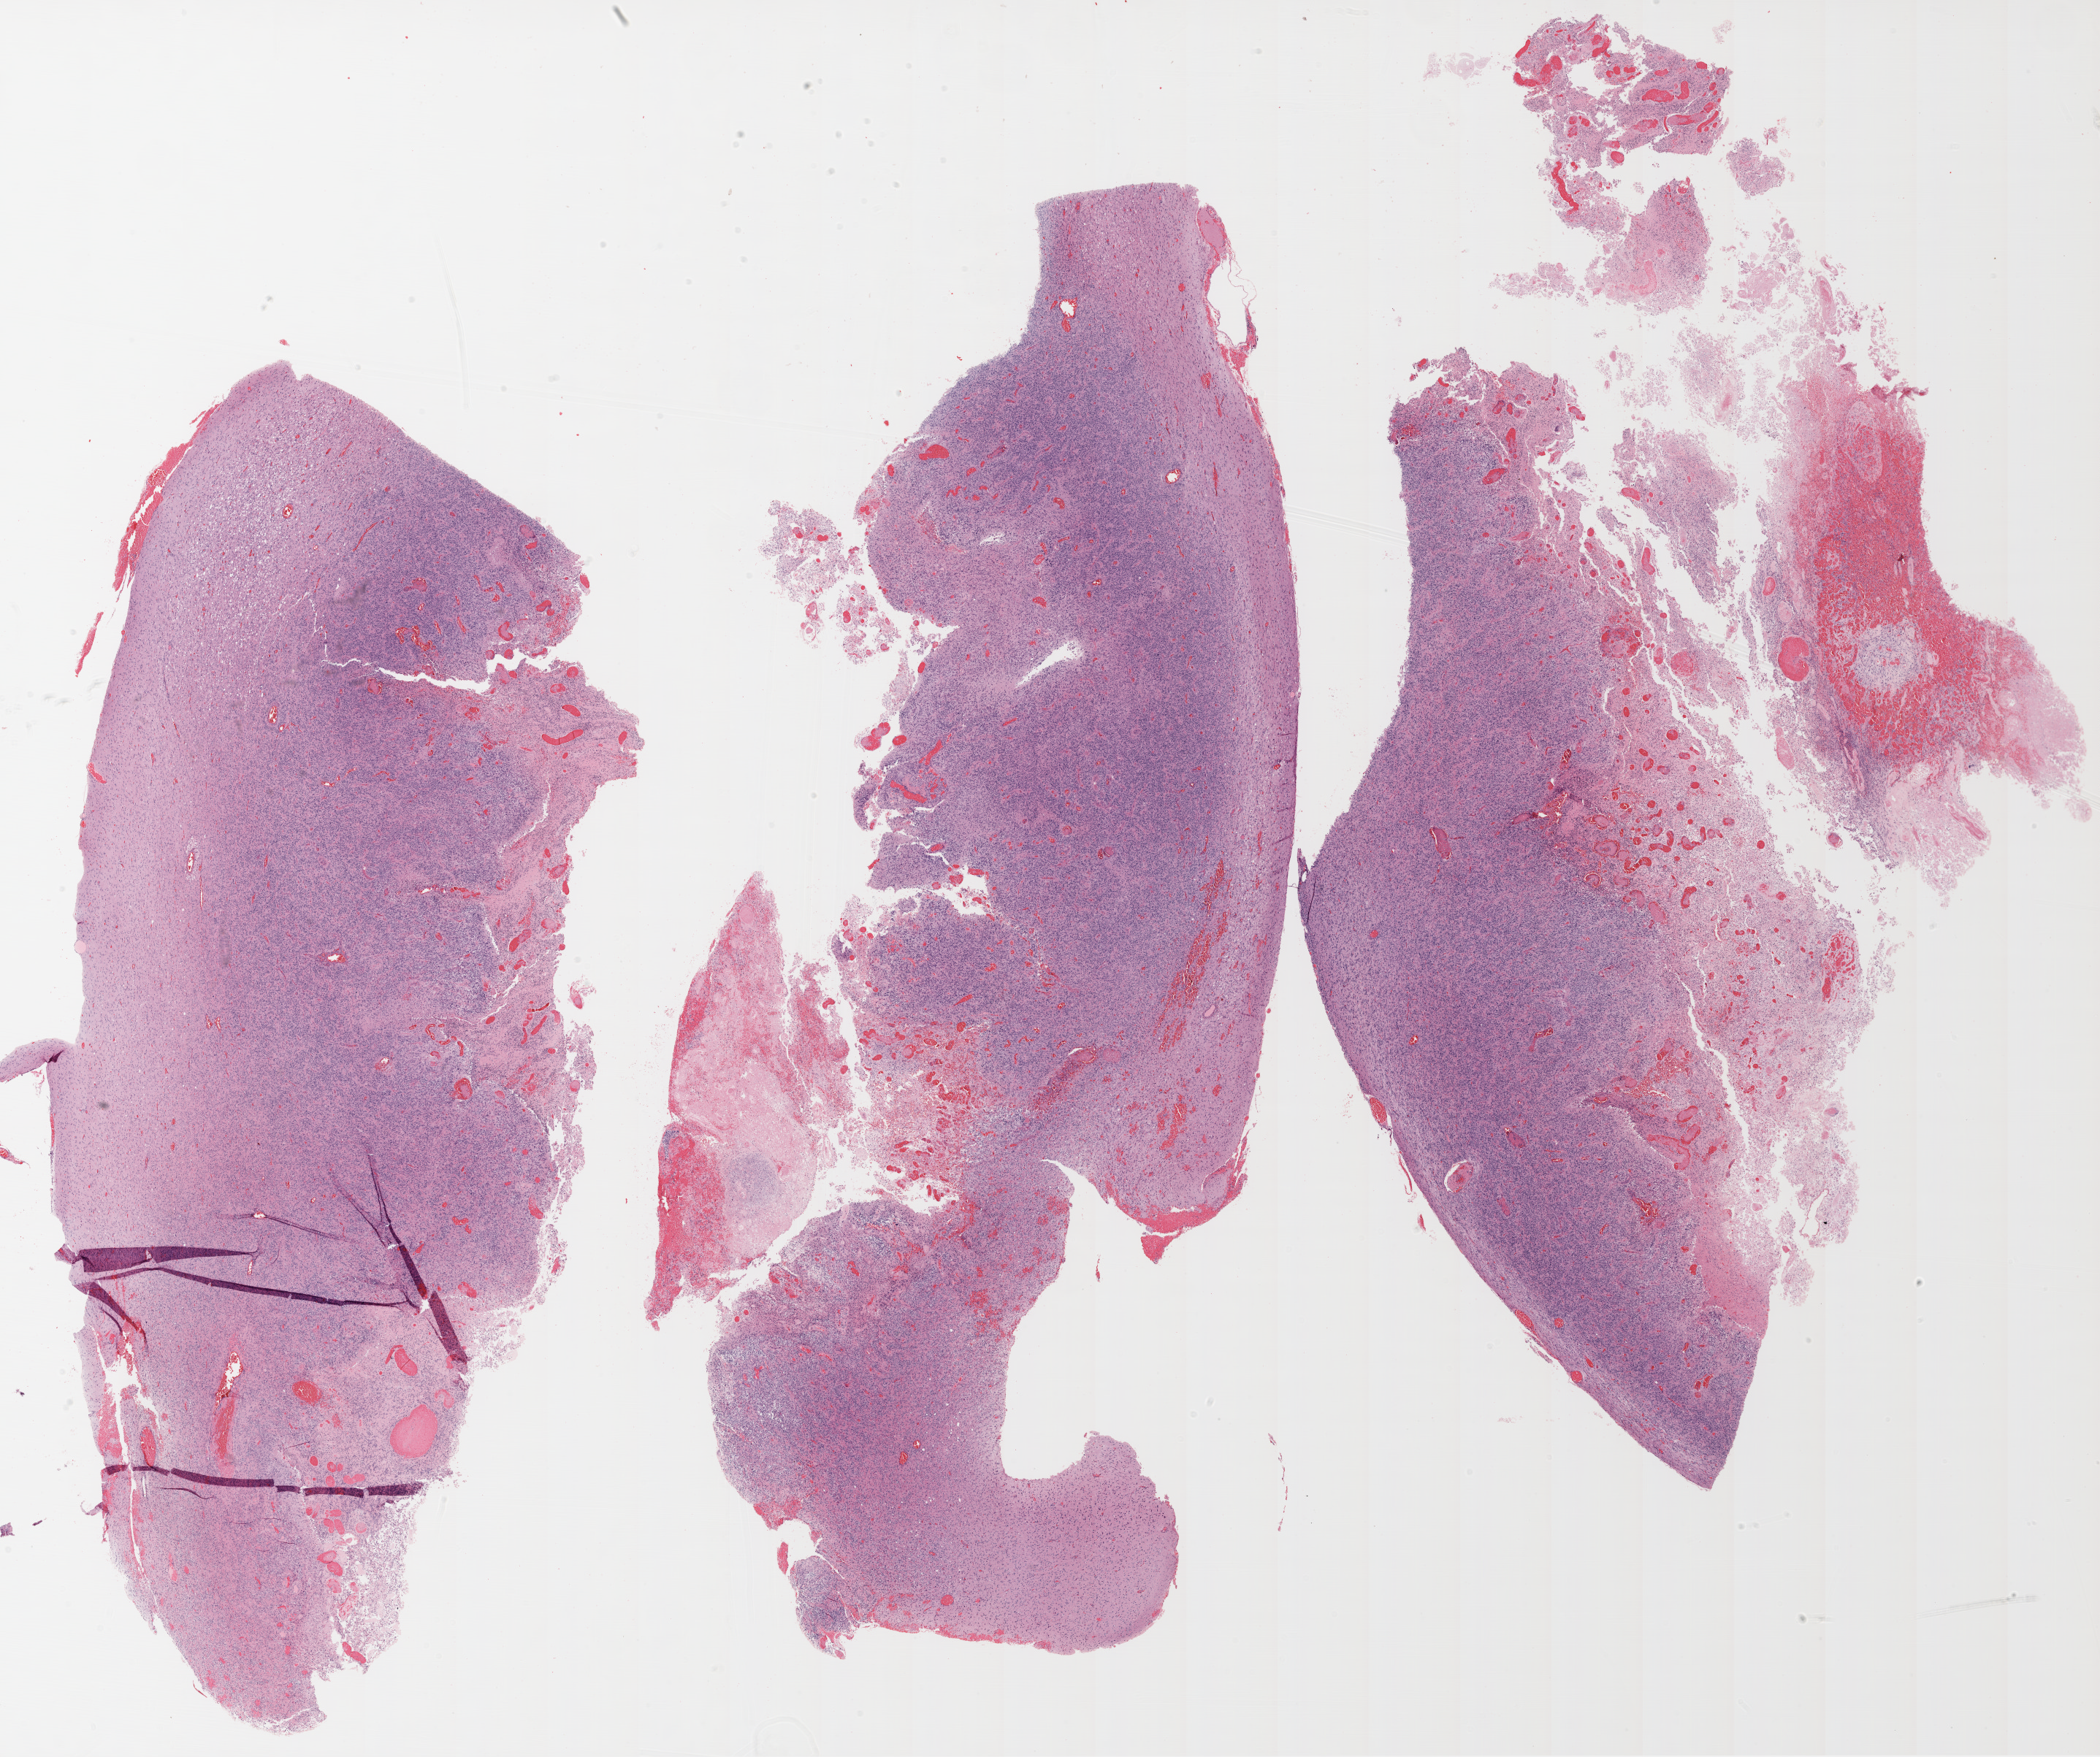
Whole-slide histology image, H&E-stained — whole scanned area (about 23.1 x 19.3 mm, slide scanned at 20x) shown as a low-resolution overview. Formalin-fixed paraffin-embedded (FFPE) diagnostic section. Brain, primary tumour sample. Male patient; age at initial diagnosis 39 years.
Pathologic diagnosis: Glioblastoma.